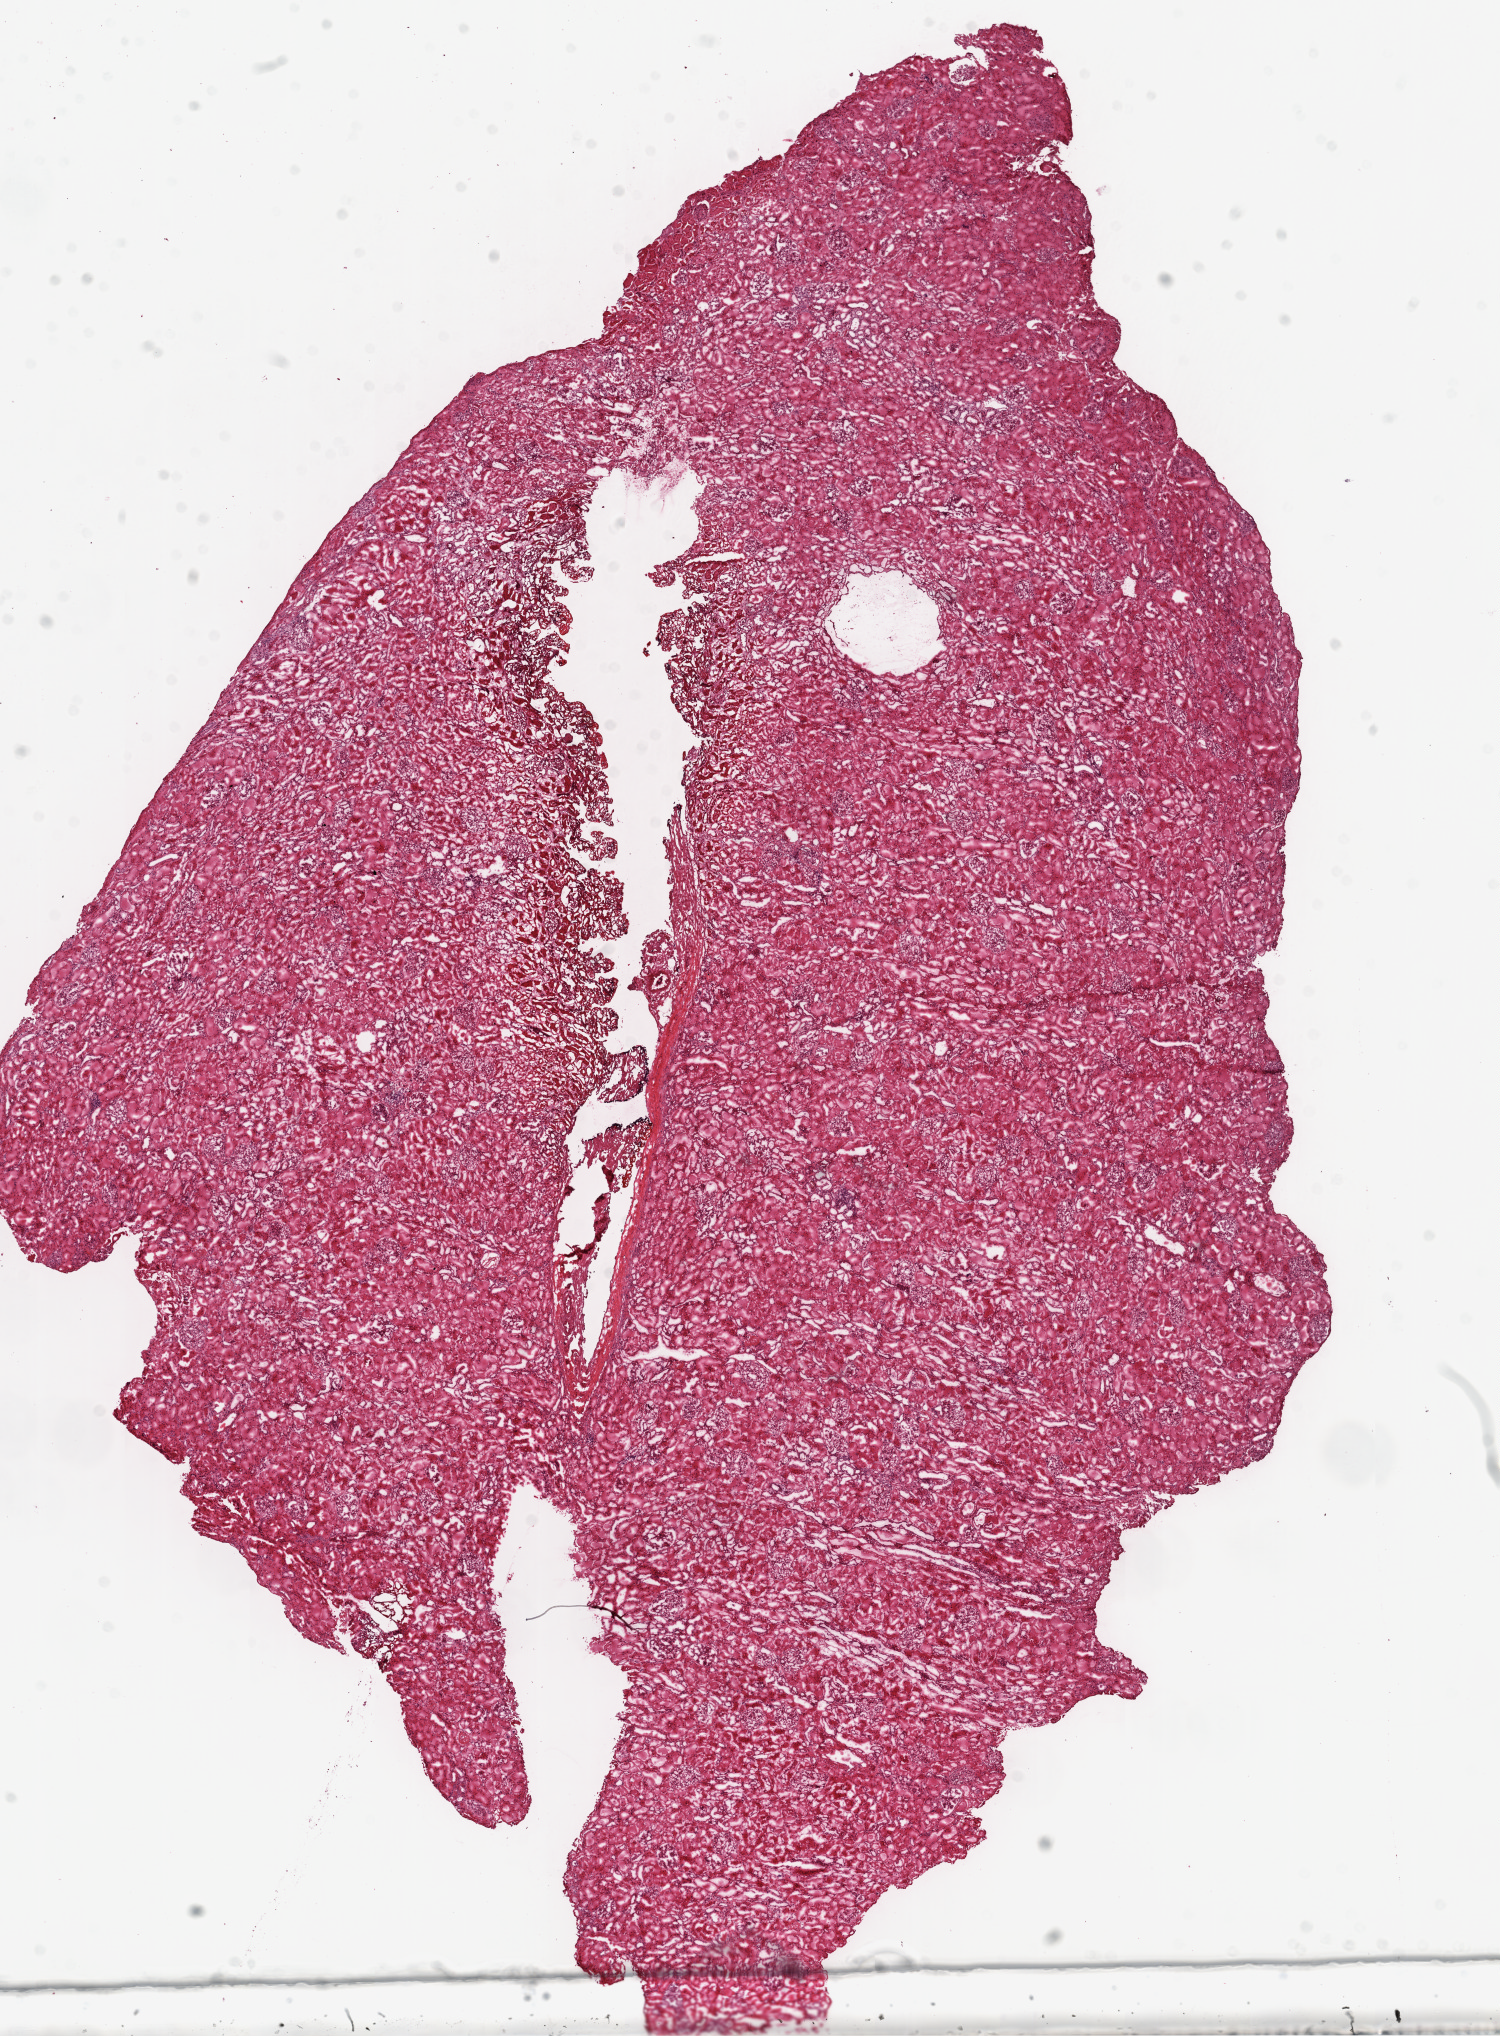
Digitized H&E-stained tissue section (whole slide), a low-resolution overview of the entire scanned area, about 12.0 x 16.3 mm, frozen section from the top of the tissue portion, sample: solid tissue normal (non-tumour tissue), kidney. Patient: female, age at initial diagnosis 45 years.
This section: solid tissue normal (non-tumour) sample from the same patient. Patient diagnosis: Clear cell adenocarcinoma, NOS.